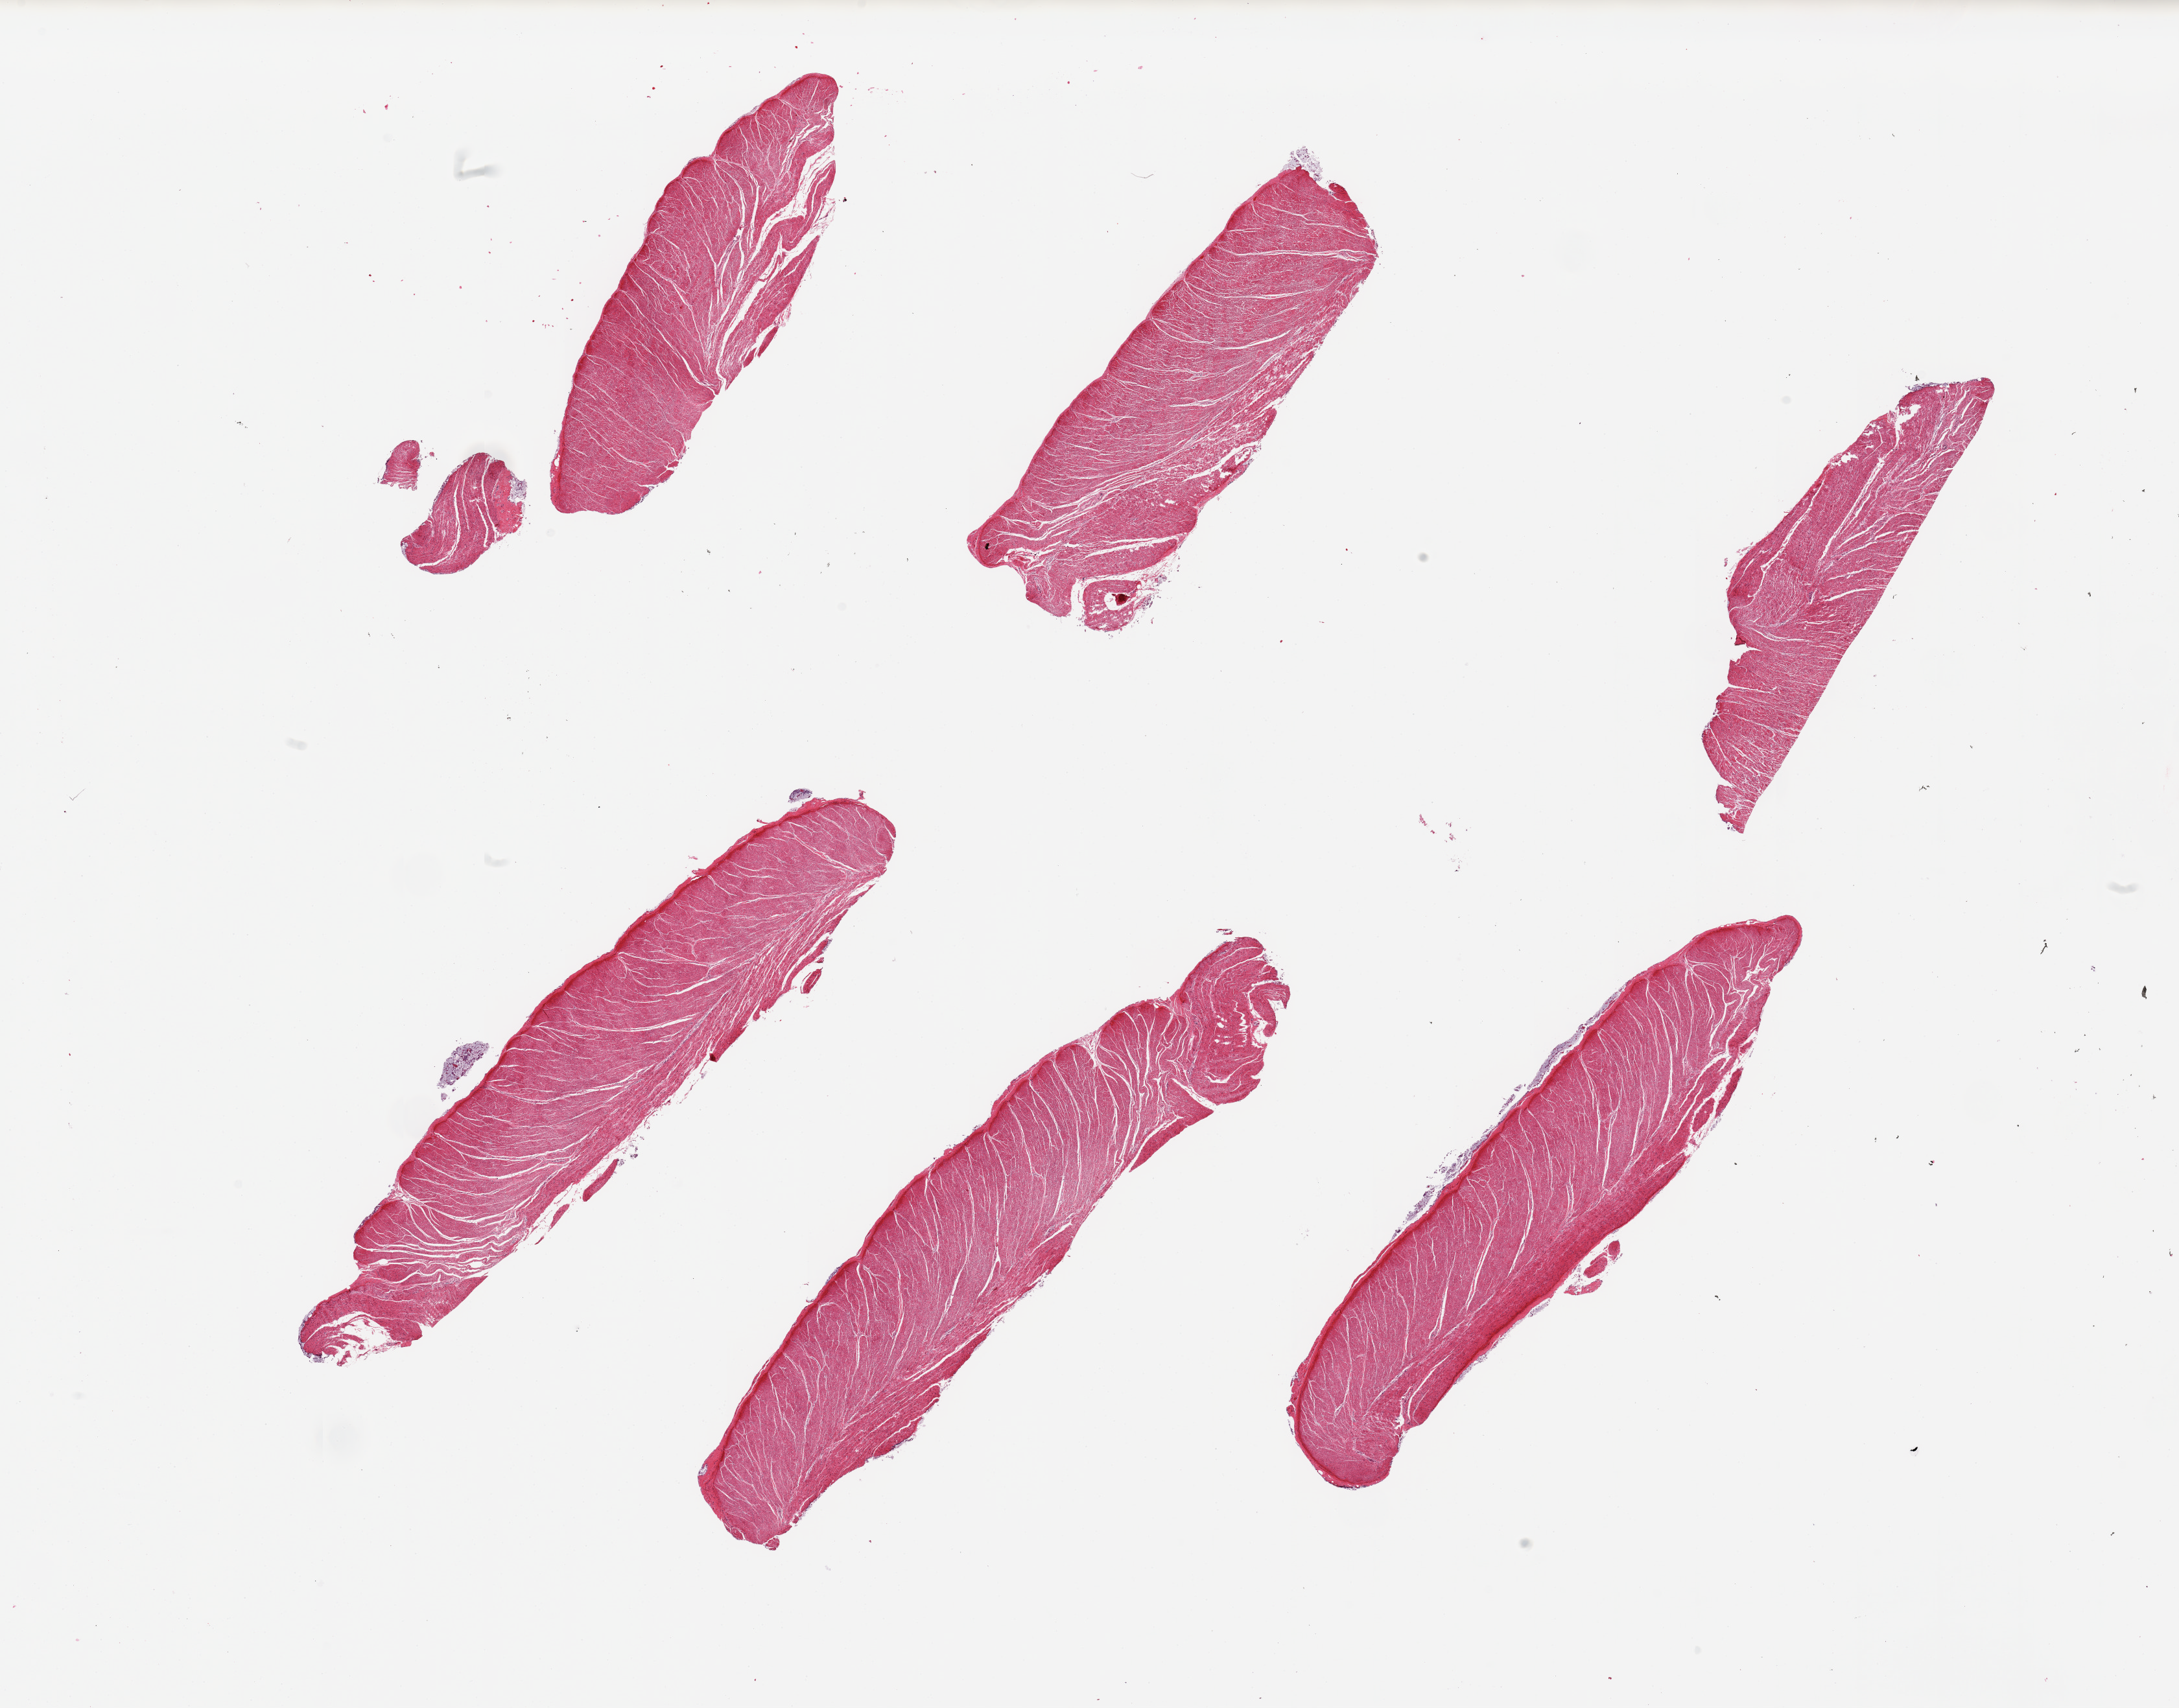
Haematoxylin and eosin whole-slide image, brightfield — shown as a low-resolution overview of the whole scanned area (about 26.6 x 20.8 mm, from a 20x scan); PAXgene-fixed paraffin-embedded (PFPE) section; sampled site (target tissue): sigmoid colon; donor tissue sample.
Review note (as recorded): 6 pieces; well dissected muscularis.